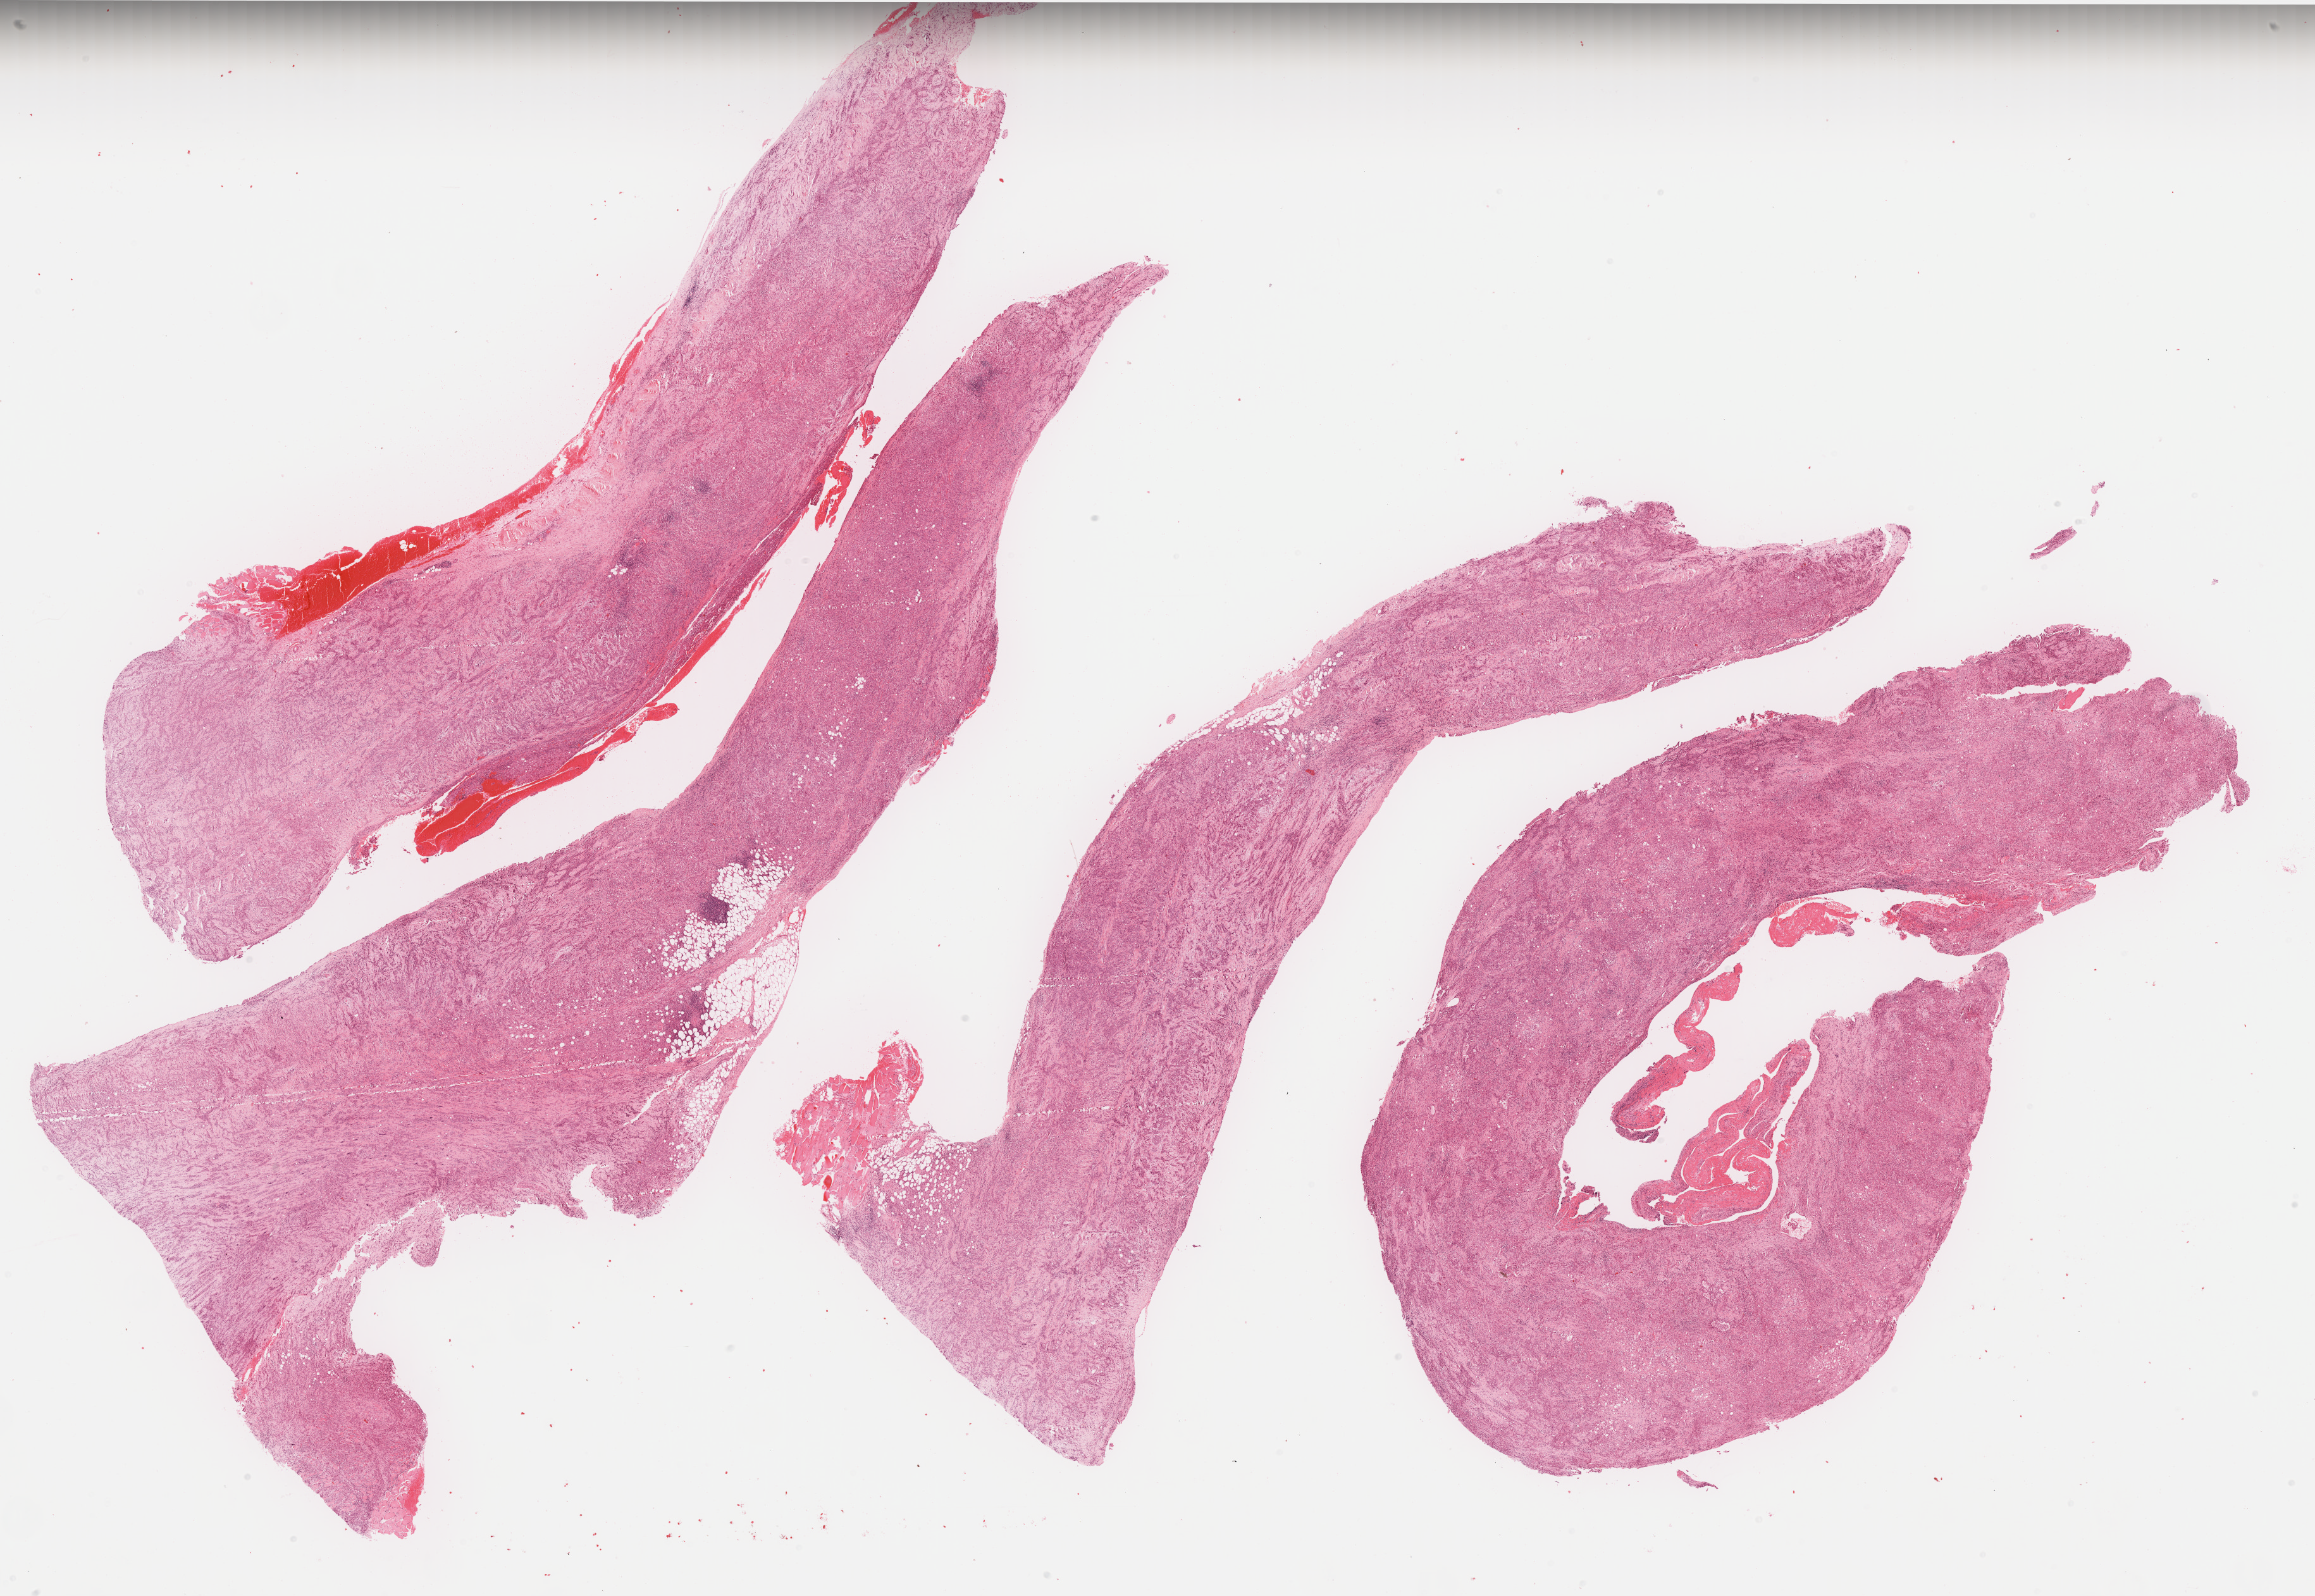
Digitized Hematoxylin and eosin (H&E) stained tissue section (whole slide), a low-resolution overview of the entire scanned area, about 29.3 x 20.2 mm (slide scanned at 40x). Formalin-fixed paraffin-embedded (FFPE) diagnostic section. Primary tumour sample from the mesothelium. Patient: male, age at initial diagnosis 66 years.
AJCC pathologic stage: III. Pathologic diagnosis: Epithelioid mesothelioma, malignant (pleura, NOS).